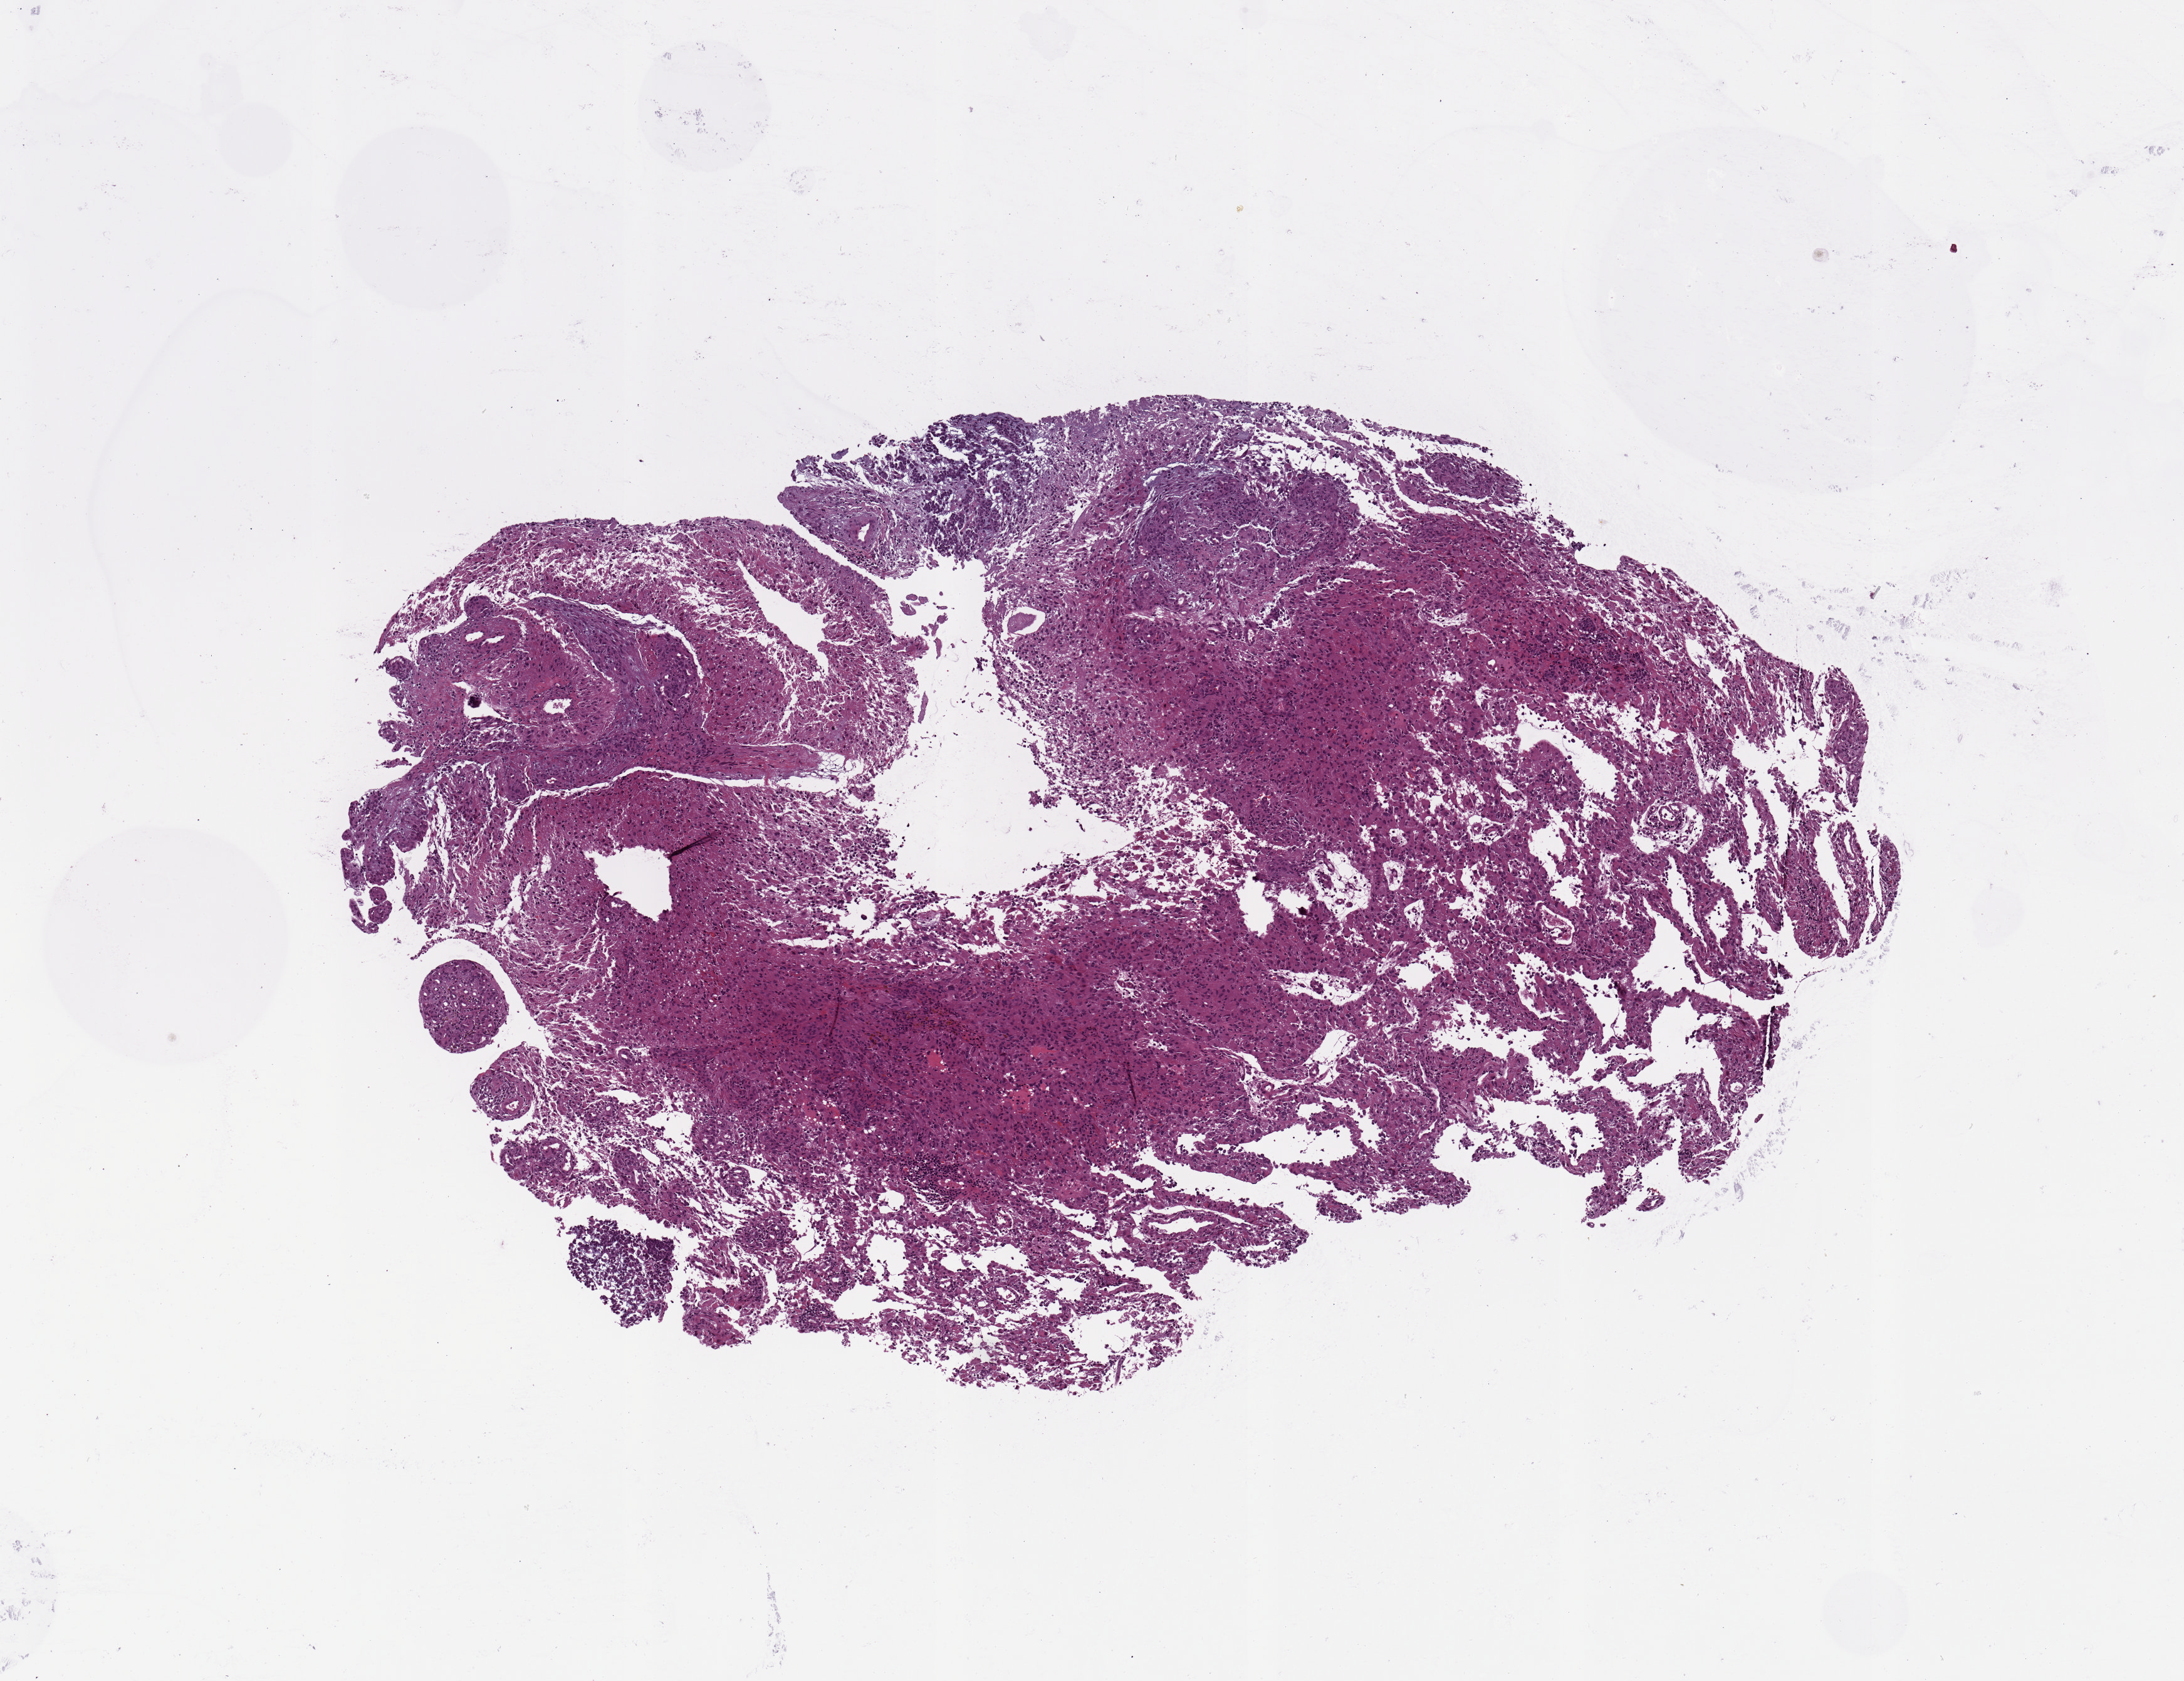
Whole-slide histology image, Hematoxylin and eosin (H&E) stained, shown as a low-resolution overview of the whole scanned area (about 6.9 x 5.3 mm, slide scanned at 20x); tumour tissue sample, sampled site: brain. Patient: male, age 53 years. Composition of this section per pathologist review: tumour nuclei 80%, necrosis 5%.
Diagnosis: Glioblastoma.